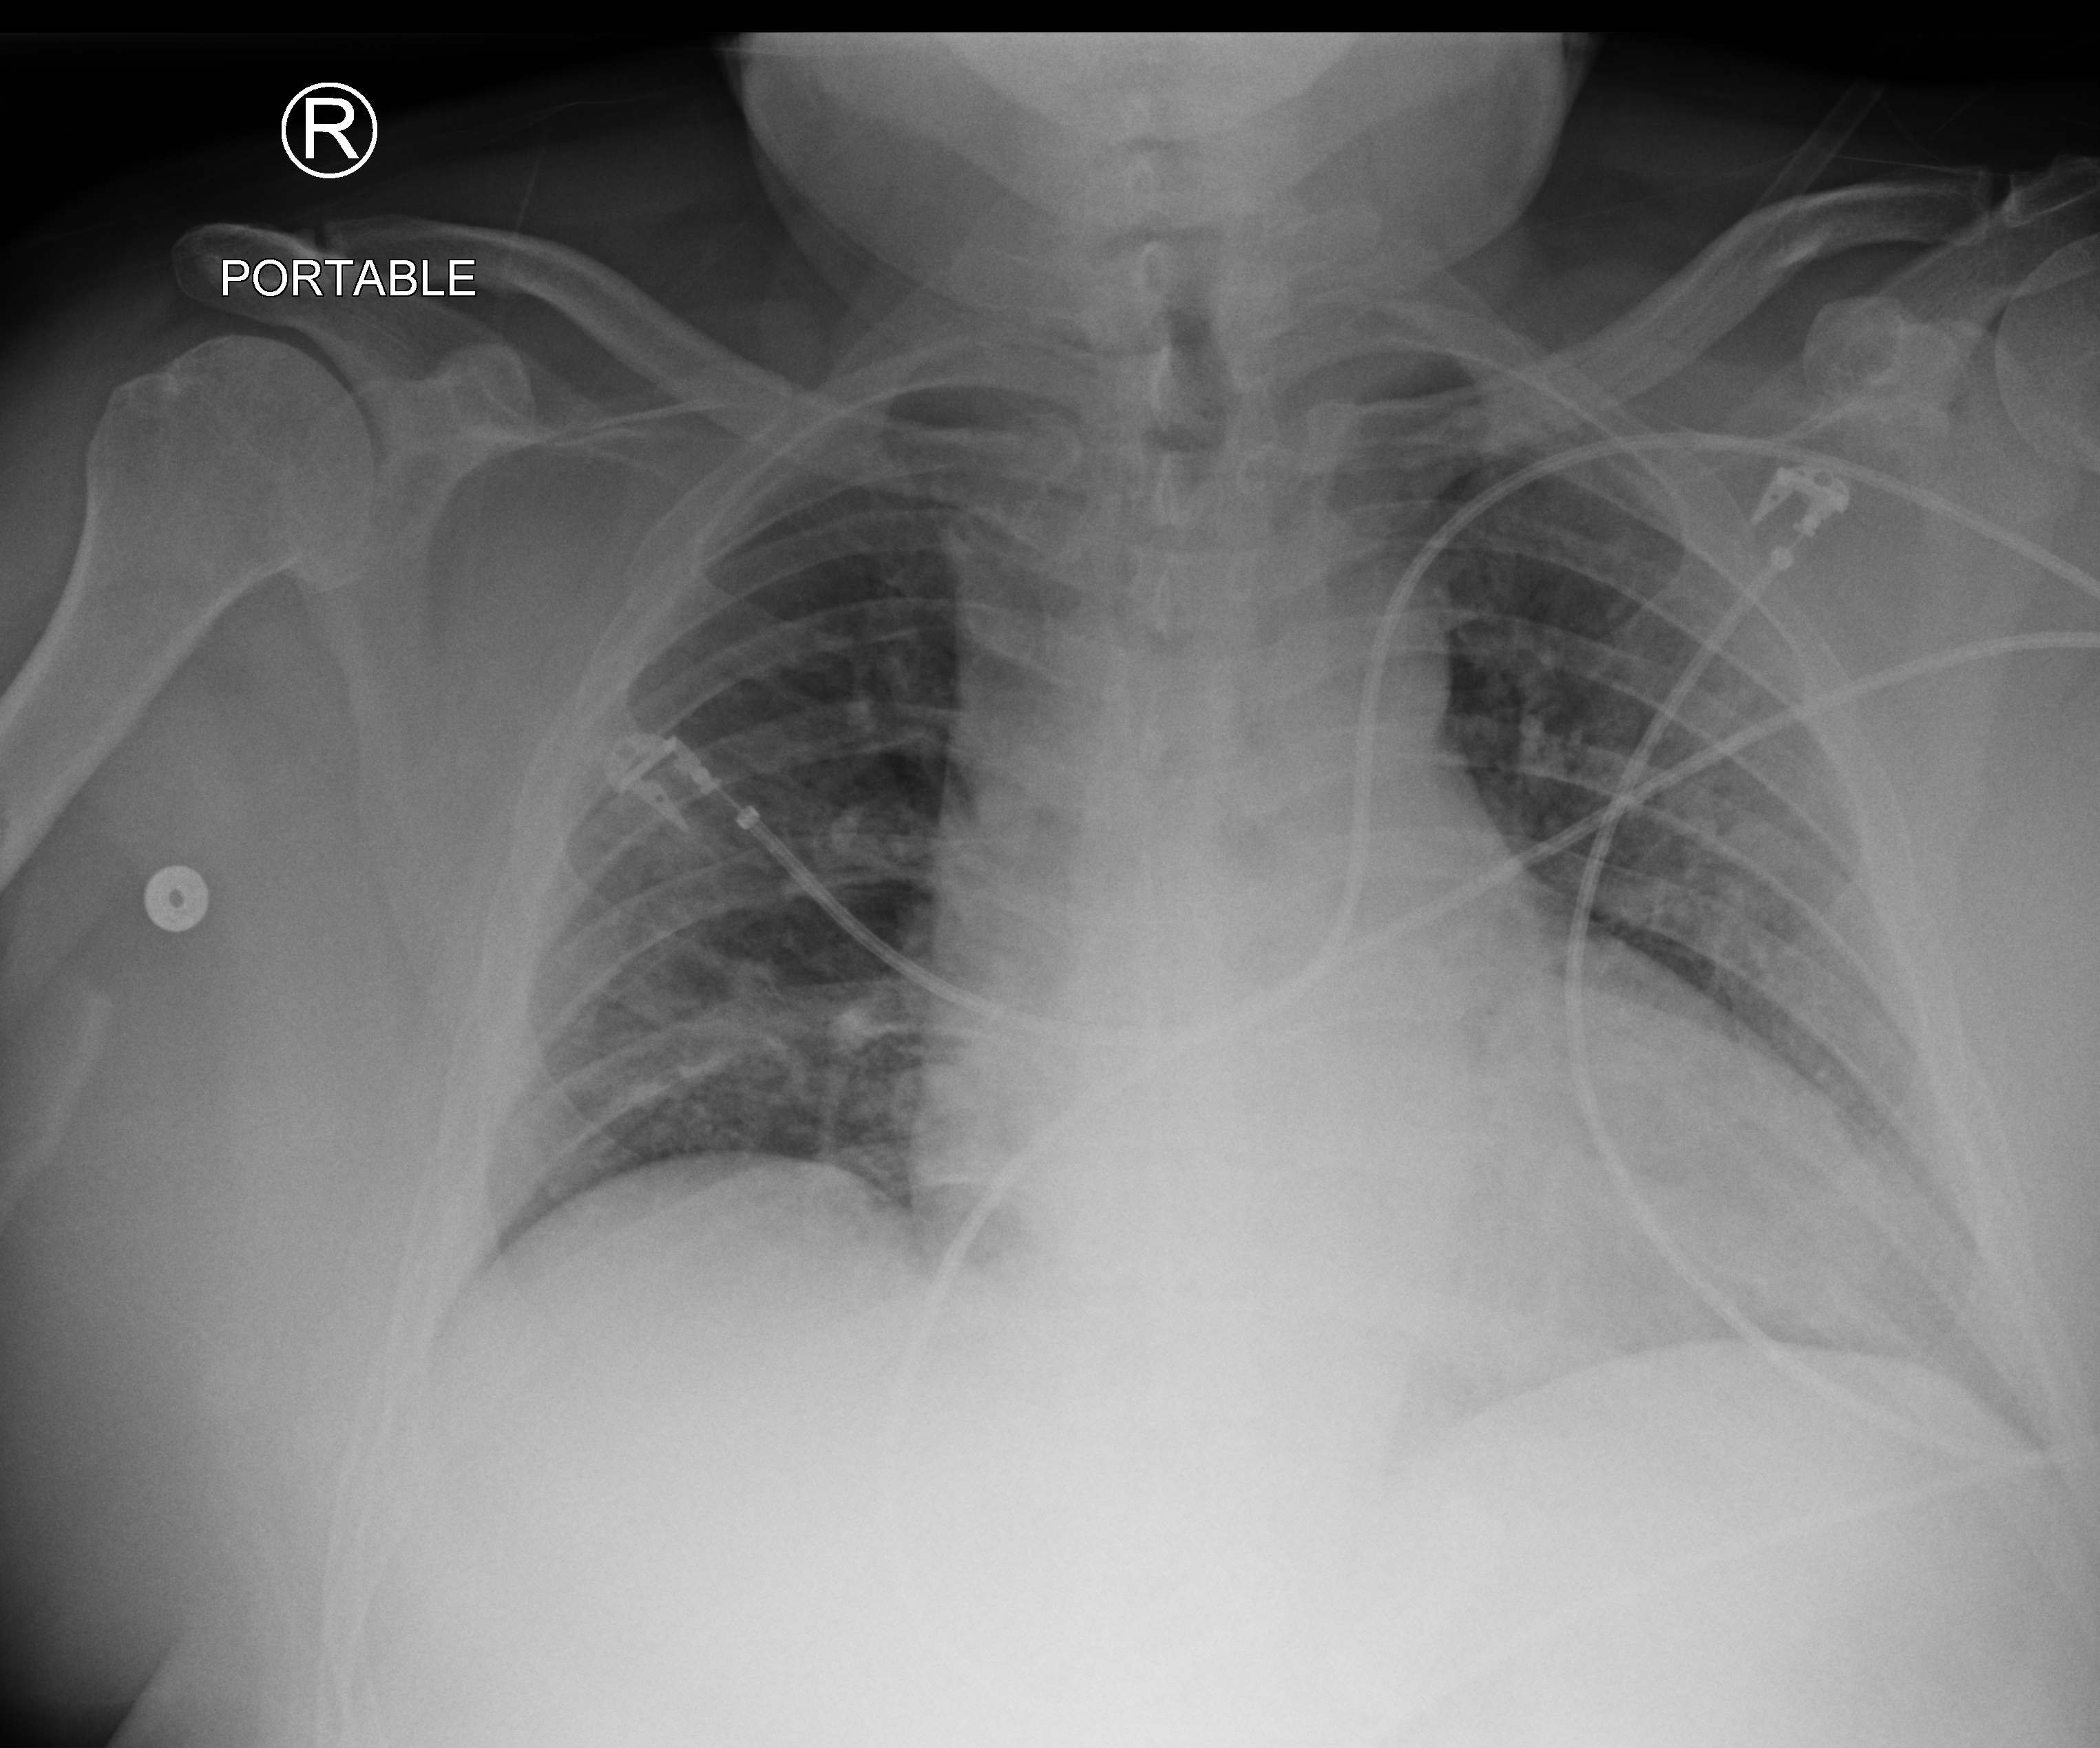
Chest X-ray (portable), anteroposterior (AP) projection. Male patient hospitalised with COVID-19, age 60–74 years.
Admission-level facts for this patient (not findings on this image; timing relative to this image not recorded): mechanically ventilated during this hospital stay: yes; admitted to intensive care during this hospital stay: yes.